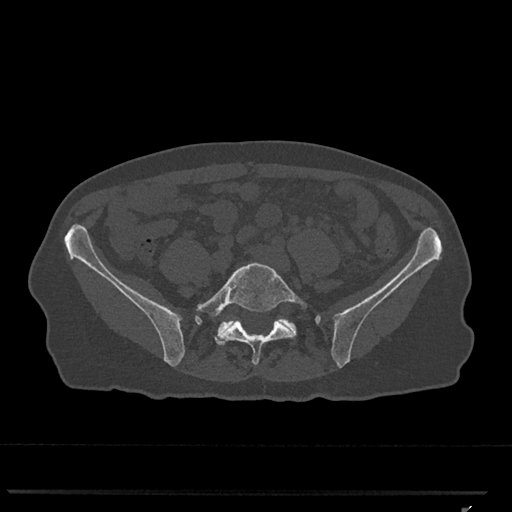
CT including the spine, one axial slice. Position 143 of 793 along the scan axis. 120 kVp. Bone window (W 1800 / L 400 HU). 0.5 mm slice thickness. 512 × 512 image matrix, field of view 380 × 380 mm. Patient: female, 62 years. From the clinical record (not read from this slice): primary cancer: renal.
Structures marked on this image (semi-automatically segmented with operator editing):
- L5 vertebra: box from (x=196, y=263) to (x=307, y=365) px